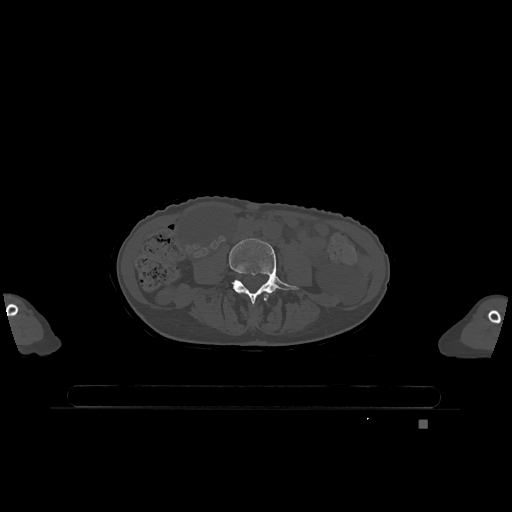
CT including the spine, one axial slice. Position 299 of 1317 along the scan axis. Bone window (W 1800 / L 400 HU). 0.5 mm slice thickness. 512 × 512 image matrix, field of view 500 × 500 mm. Patient: female, 74 years. Case-level facts recorded for this patient, not image findings: primary cancer: lung.
Outlined on this slice (semi-automatically segmented with operator editing):
- L3 vertebra: bounding box <263,293,270,301> (left, top, right, bottom; pixels)
- L4 vertebra: <229,239,299,304>